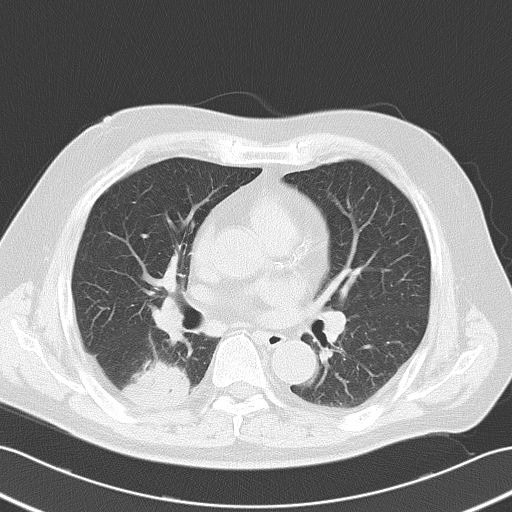
Chest CT, one axial slice; 120 kVp; lung window (W 1500 / L -600 HU); 512 × 512 image matrix. Patient: male, 70 years. Case-level facts recorded for this patient, not image findings: clinical TNM (as recorded): T2 N0 M0; histopathological grade: G2.
Structures marked on this image (rectangle marked by the reading radiologist):
- lung tumour (recorded histology: adenocarcinoma): box from (x=122, y=348) to (x=195, y=421) px